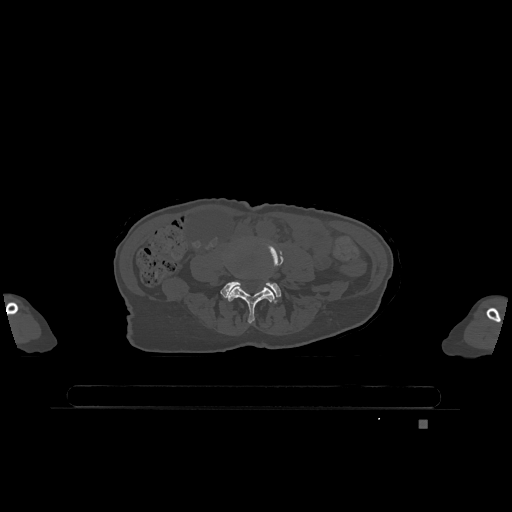
CT including the spine, one axial slice. Slice 277 of 1317 in the series (ordered by position). Bone window (W 1800 / L 400 HU). 0.5 mm slice thickness. 512 × 512 image matrix. Female patient, age 74 years. From the clinical record (not read from this slice): primary cancer: lung.
Annotated regions visible in this slice (semi-automatic segmentation, software-assisted and operator-edited):
- L4 vertebra: box from (x=228, y=243) to (x=283, y=323) px
- L5 vertebra: (x=221, y=281)–(x=281, y=301)